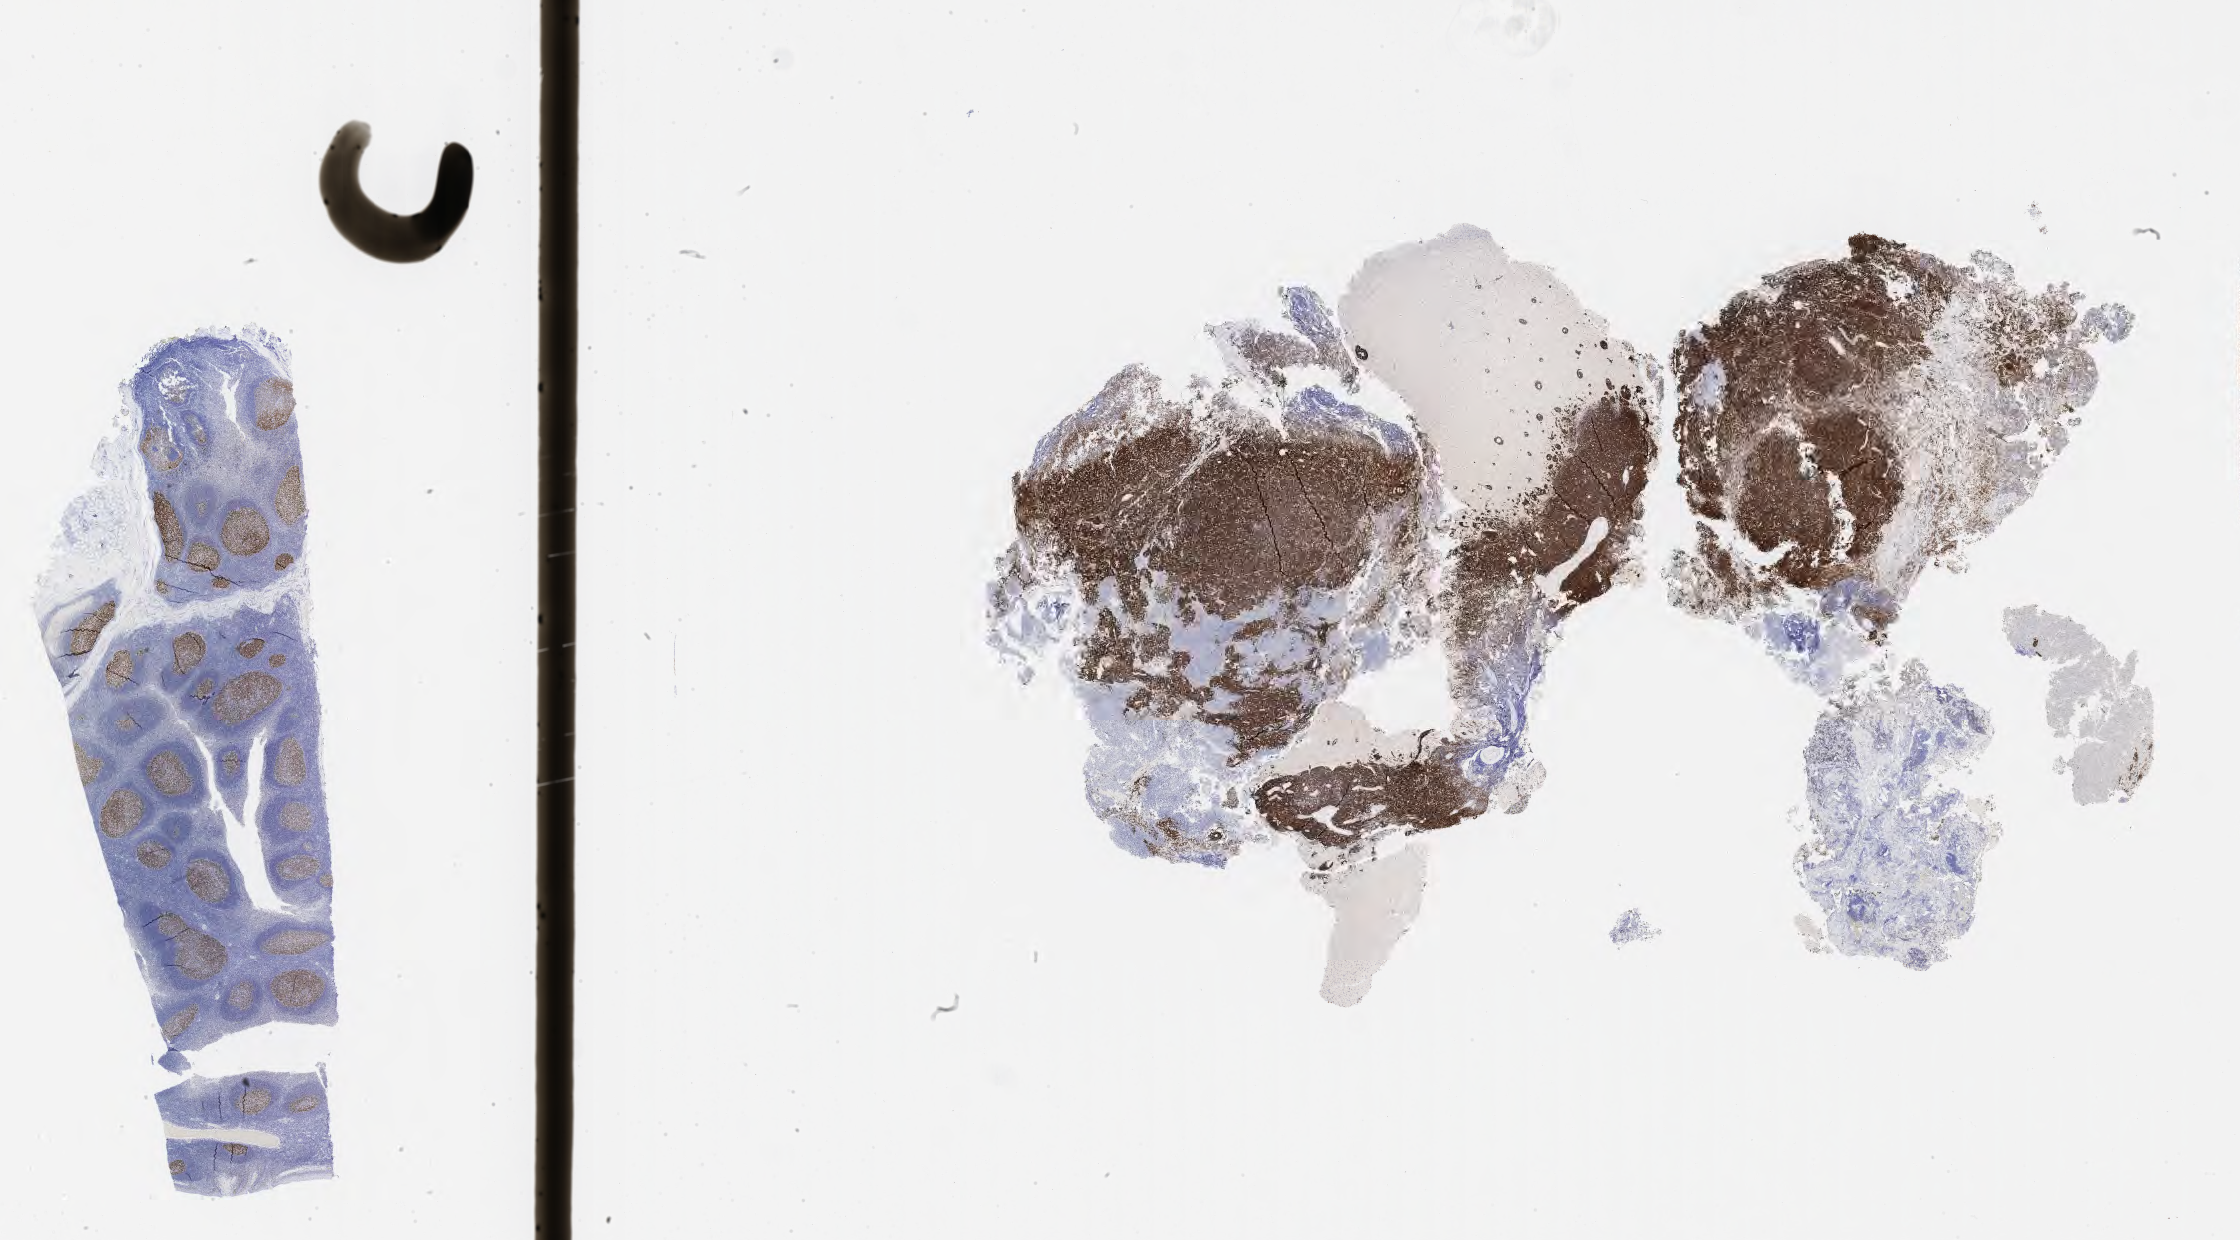
Whole-slide image, immunohistochemical stain for BCL6, low-resolution overview of the scanned area, about 36.2 x 20.1 mm, tumor tissue. Female patient, aged 73.
Histologic diagnosis: Burkitt lymphoma, NOS.